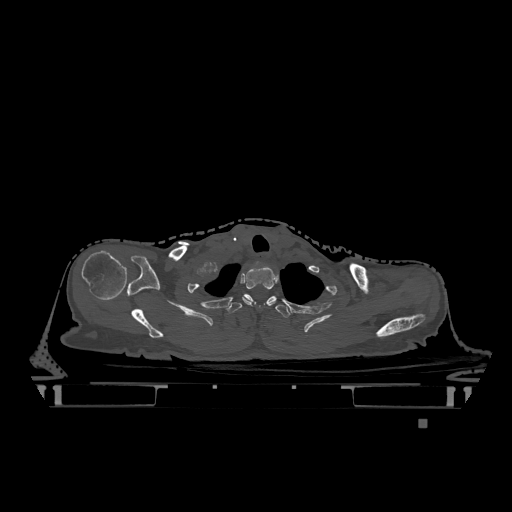
CT including the spine, one axial slice. Position 985 of 1317 along the scan axis. Bone window (W 1800 / L 400 HU). 0.5 mm slice thickness. 512 × 512 image matrix, field of view 500 × 500 mm. Female patient, age 74 years. From the clinical record (not read from this slice): primary cancer: lung; vertebrae with lytic lesions (as recorded): T1, T4, T5, T6, L4, L5.
Outlined on this slice (semi-automatic segmentation, software-assisted and operator-edited):
- T1 vertebra: bounding box [x1, y1, x2, y2] px = [242, 266, 277, 306]
- T2 vertebra: [227, 294, 290, 318]